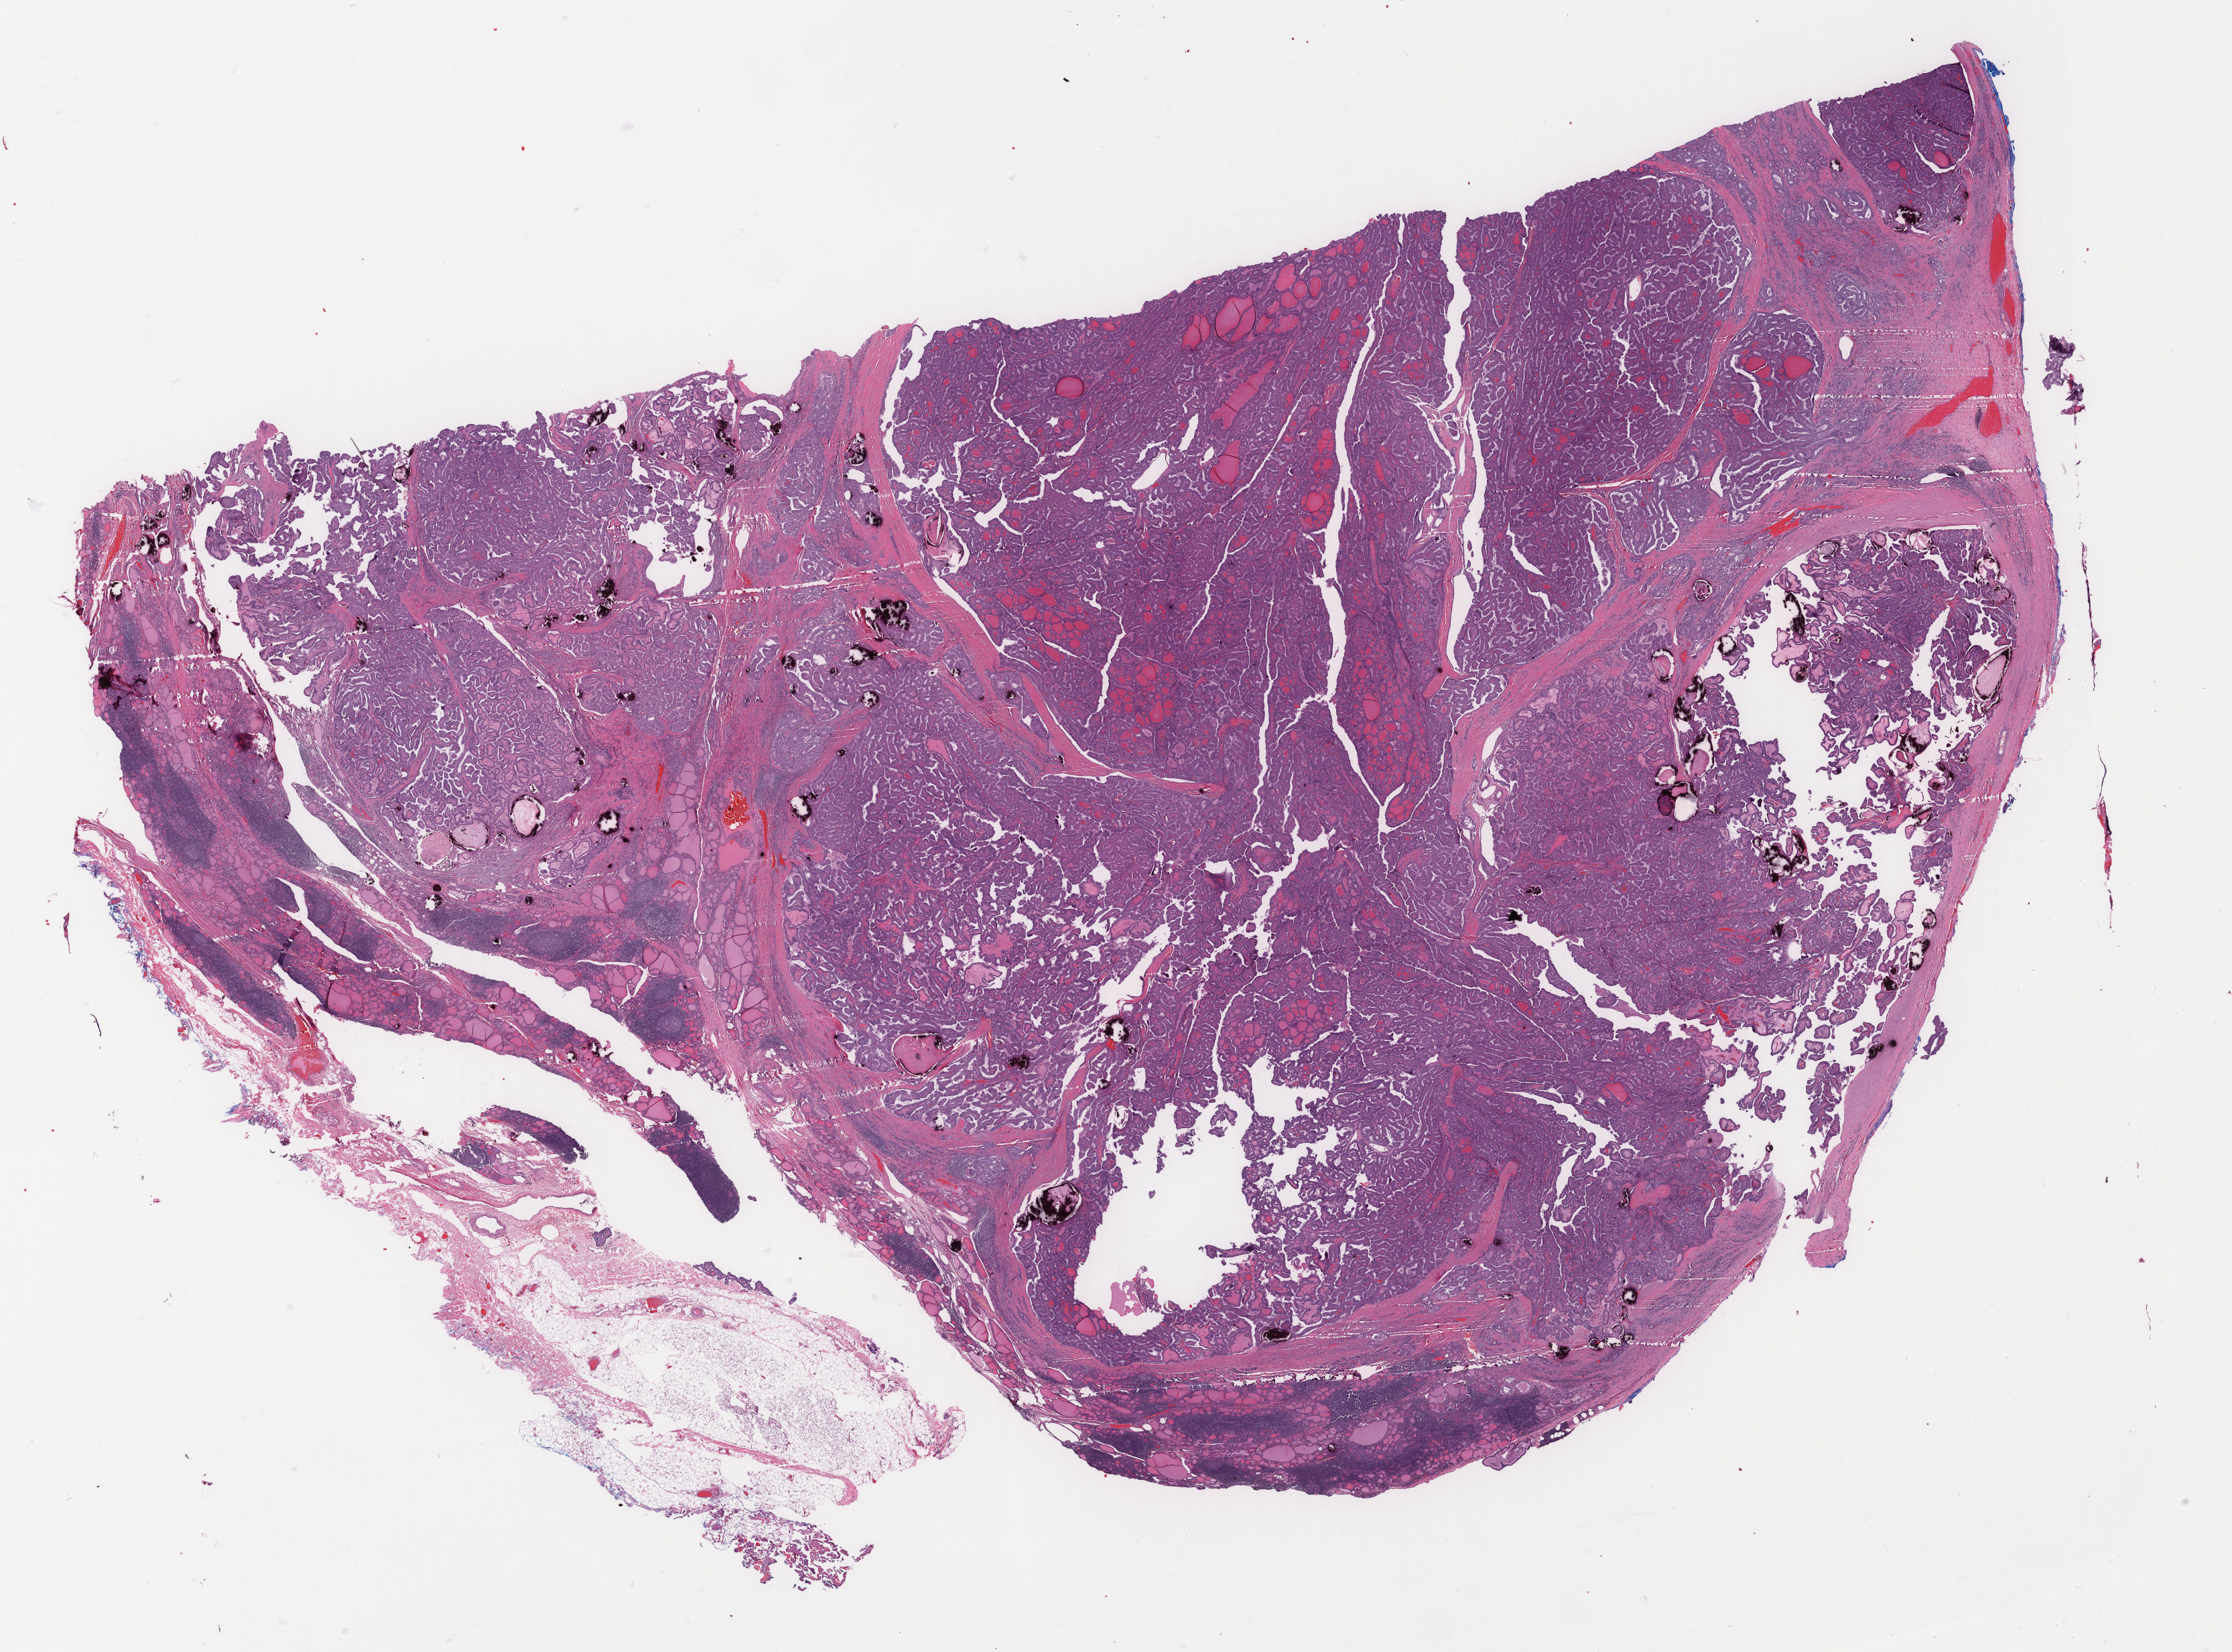
Digitized H&E-stained tissue section (whole slide) — shown as a low-resolution overview of the whole scanned area (about 26.4 x 19.6 mm, slide scanned at 40x). Formalin-fixed paraffin-embedded (FFPE) diagnostic section. Primary tumour sample from the thyroid. Patient: female, age at initial diagnosis 21 years.
* AJCC pathologic stage: I (7th edition)
* TNM: T3 N1a M0
* lymph nodes positive (case pathology): 8 of 20 examined
* histologic diagnosis: Papillary adenocarcinoma, NOS (thyroid gland)